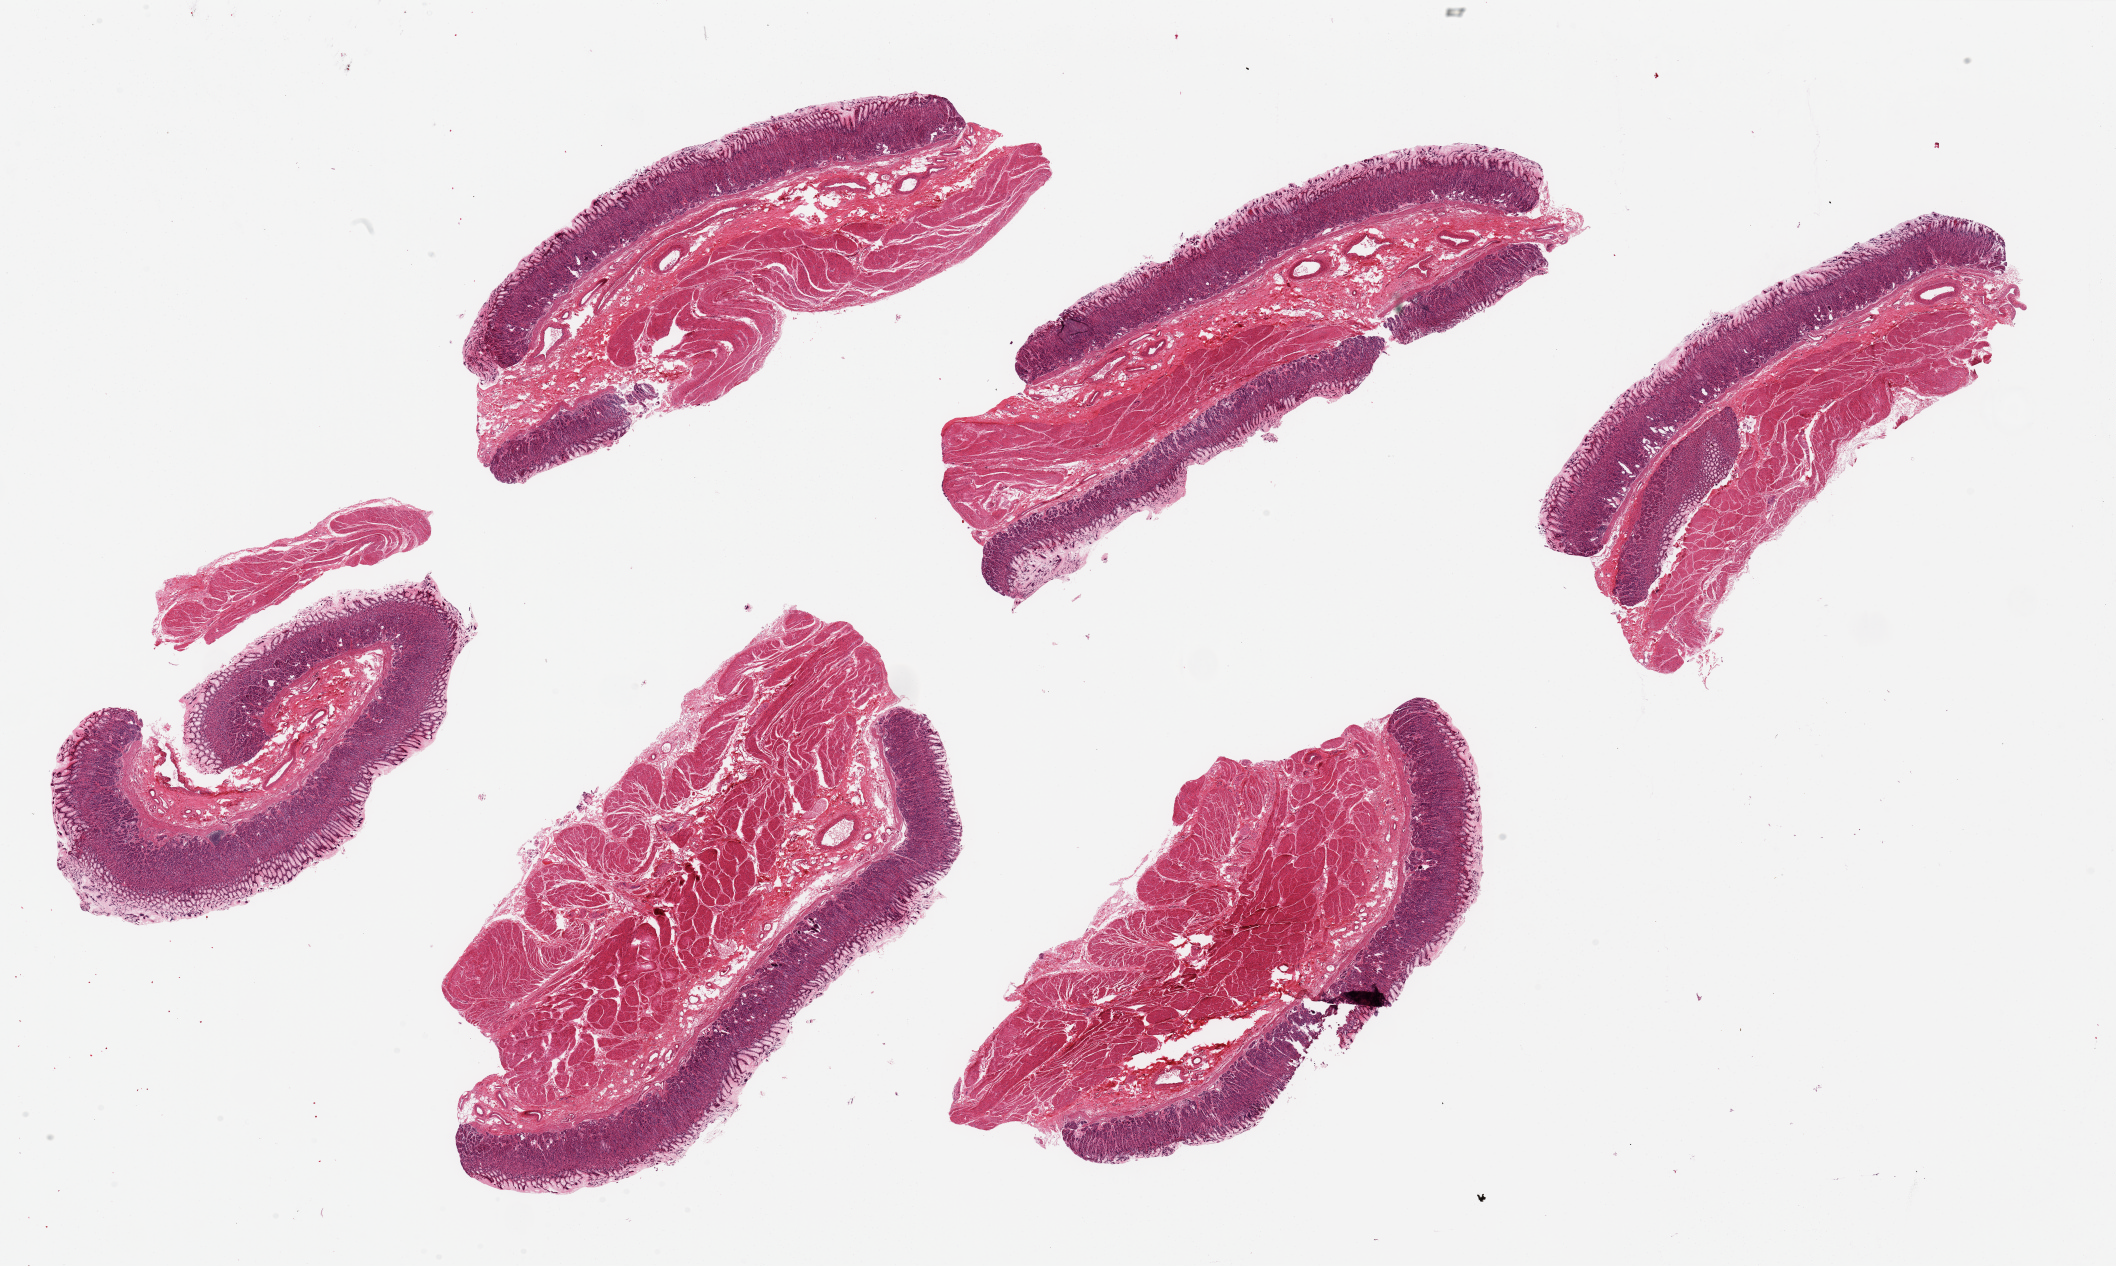
Haematoxylin and eosin whole-slide image, shown as a low-resolution overview of the whole scanned area (about 33.5 x 20.0 mm), PAXgene-fixed paraffin-embedded (PFPE) section, section of stomach (target tissue), donor tissue sample. Female donor.
Reviewer comment on this tissue sample: 6 pieces, ~10x4 mm; very good and abundant mucosa up to 1 mm thick.